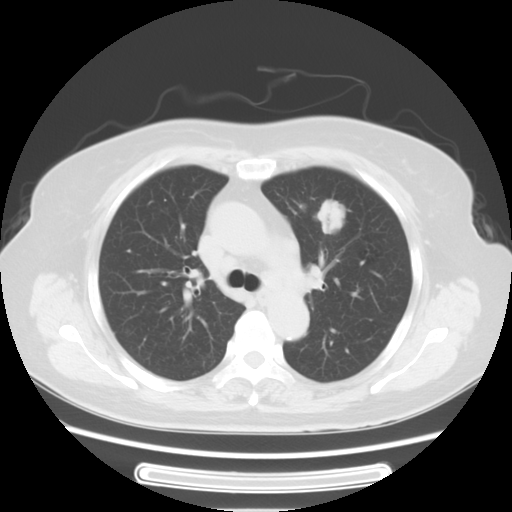
Chest CT, one axial slice. Slice 41 of 57 in the series (ordered by position). Reconstruction kernel STANDARD. Lung window (W 1500 / L -600 HU). 5 mm slice thickness. 512 × 512 image matrix. Female patient, age 77 years. From the clinical record (not read from this slice): clinical TNM (as recorded): T1c N3 M0; histopathological grade: G2-3.
Outlined on this slice (rectangle marked by the reading radiologist):
- lung tumour (recorded histology: adenocarcinoma): bounding box [x1, y1, x2, y2] px = [313, 189, 347, 240]